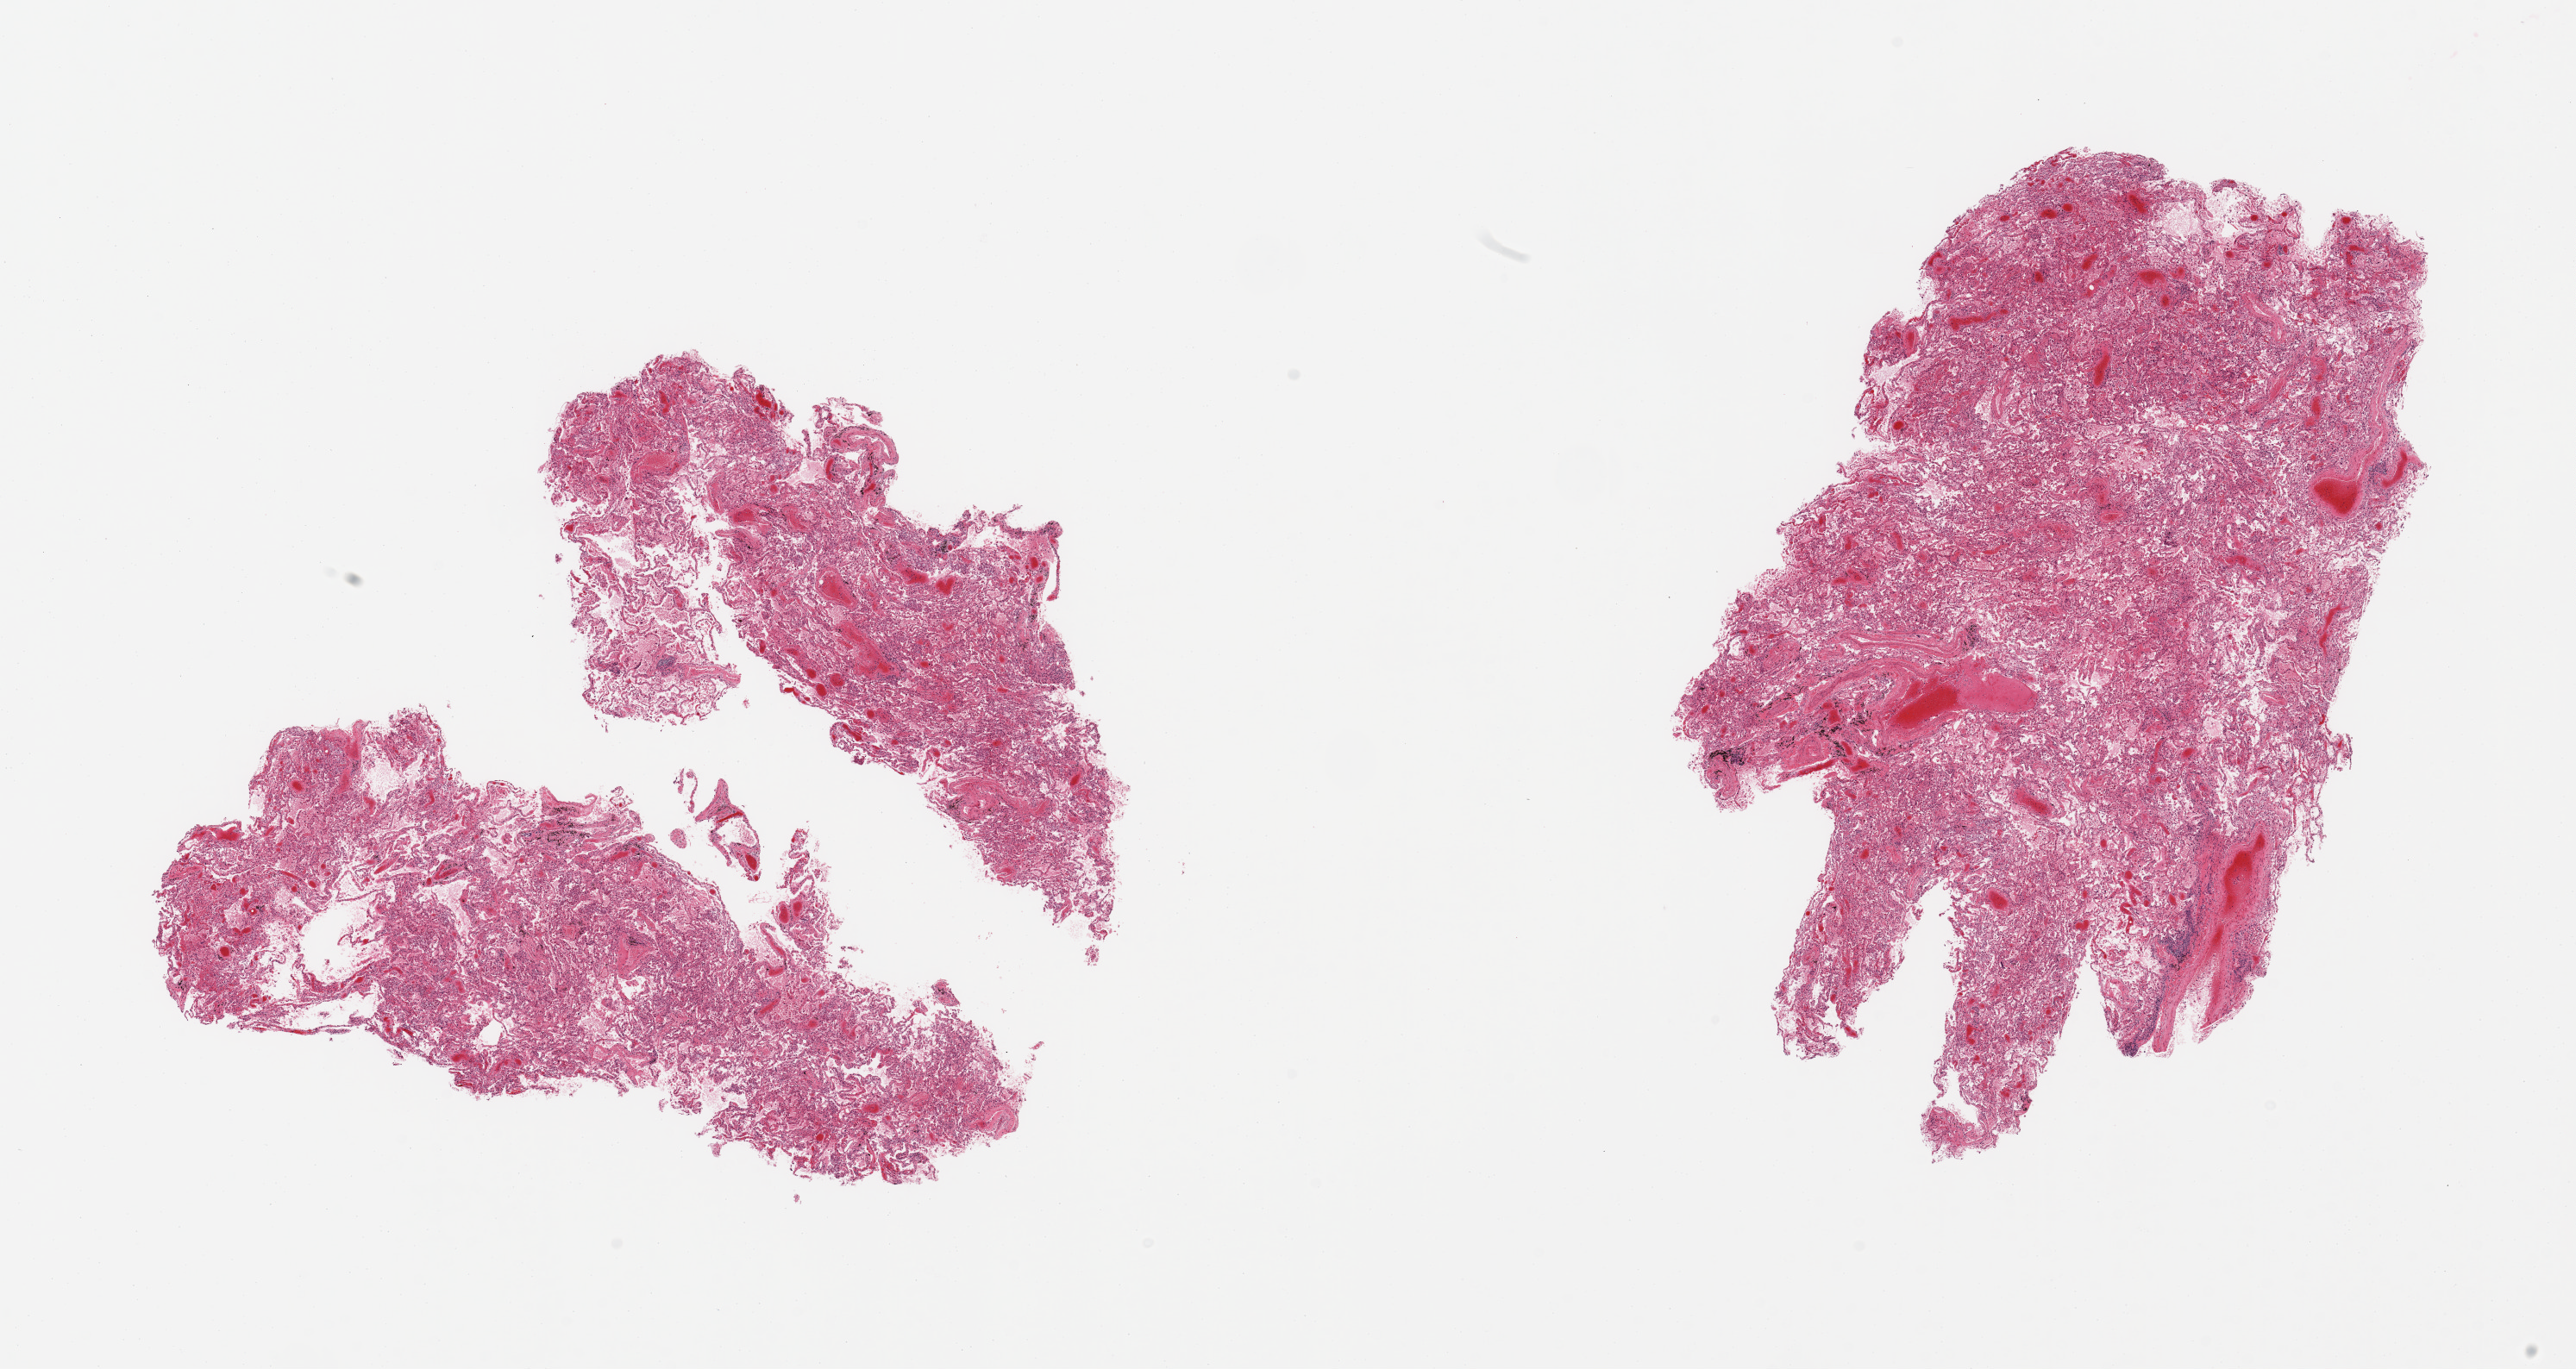
Hematoxylin and eosin (H&E) whole-slide image, brightfield — a low-resolution overview of the entire scanned area, about 23.6 x 12.6 mm; PAXgene-fixed, paraffin-embedded tissue; sampled site (target tissue): lung; tissue donor sample. Donor sex: male.
• reviewer comment on this tissue sample: 2 pieces; pulmonary edema with alveolar macrophages; moderate congestion